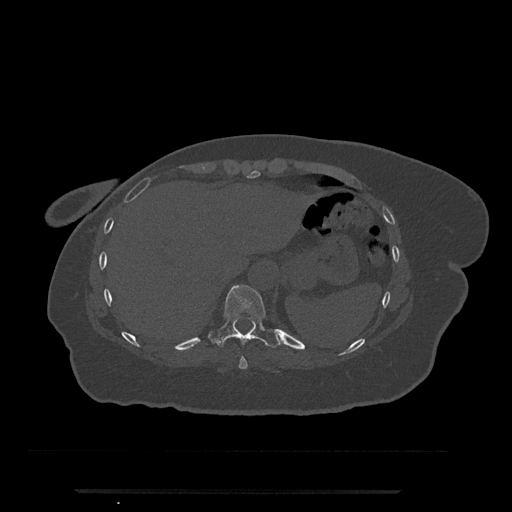
CT including the spine, one axial slice; slice 296 of 797 in the series (ordered by position); reconstruction kernel Br40s/3; bone window (W 1800 / L 400 HU); 0.5 mm slice thickness; 512 × 512 image matrix, field of view 440 × 440 mm. Female patient, age 51 years. Case-level facts recorded for this patient, not image findings: primary cancer: neuro; vertebrae with lytic lesions (as recorded): T8.
Outlined on this slice (semi-automatic segmentation, software-assisted and operator-edited):
- T10 vertebra: bounding box <211,285,280,348> (left, top, right, bottom; pixels)
- T9 vertebra: <238,355,248,369>